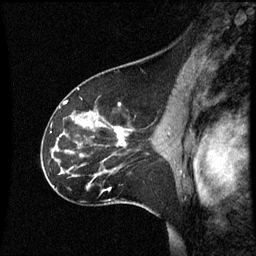
Breast MRI (dynamic contrast-enhanced), one sagittal slice; slice 37 of 60 in the series (ordered by position); dynamic contrast-enhanced series, image 2 of 3 at this slice position (ordered by acquisition); 1.5 T; TE 4.2 ms, TR 8.9 ms; 256 × 256 image matrix. Patient: female, 45 years. Case-level facts recorded for this patient, not image findings: setting: breast cancer imaged before/during neoadjuvant chemotherapy; receptor status: HR-positive, HER2-negative.
Structures marked on this image (semi-automatic segmentation, software-assisted and operator-edited):
- analysis volume of interest (the breast-tissue region the enhancement analysis was run in; not a lesion): bounding box (x1, y1, x2, y2) in pixels: (46, 94, 171, 205)
- tumour enhancement mask (voxels above the 70 % enhancement threshold inside the analysis volume of interest): (112, 126, 125, 143)